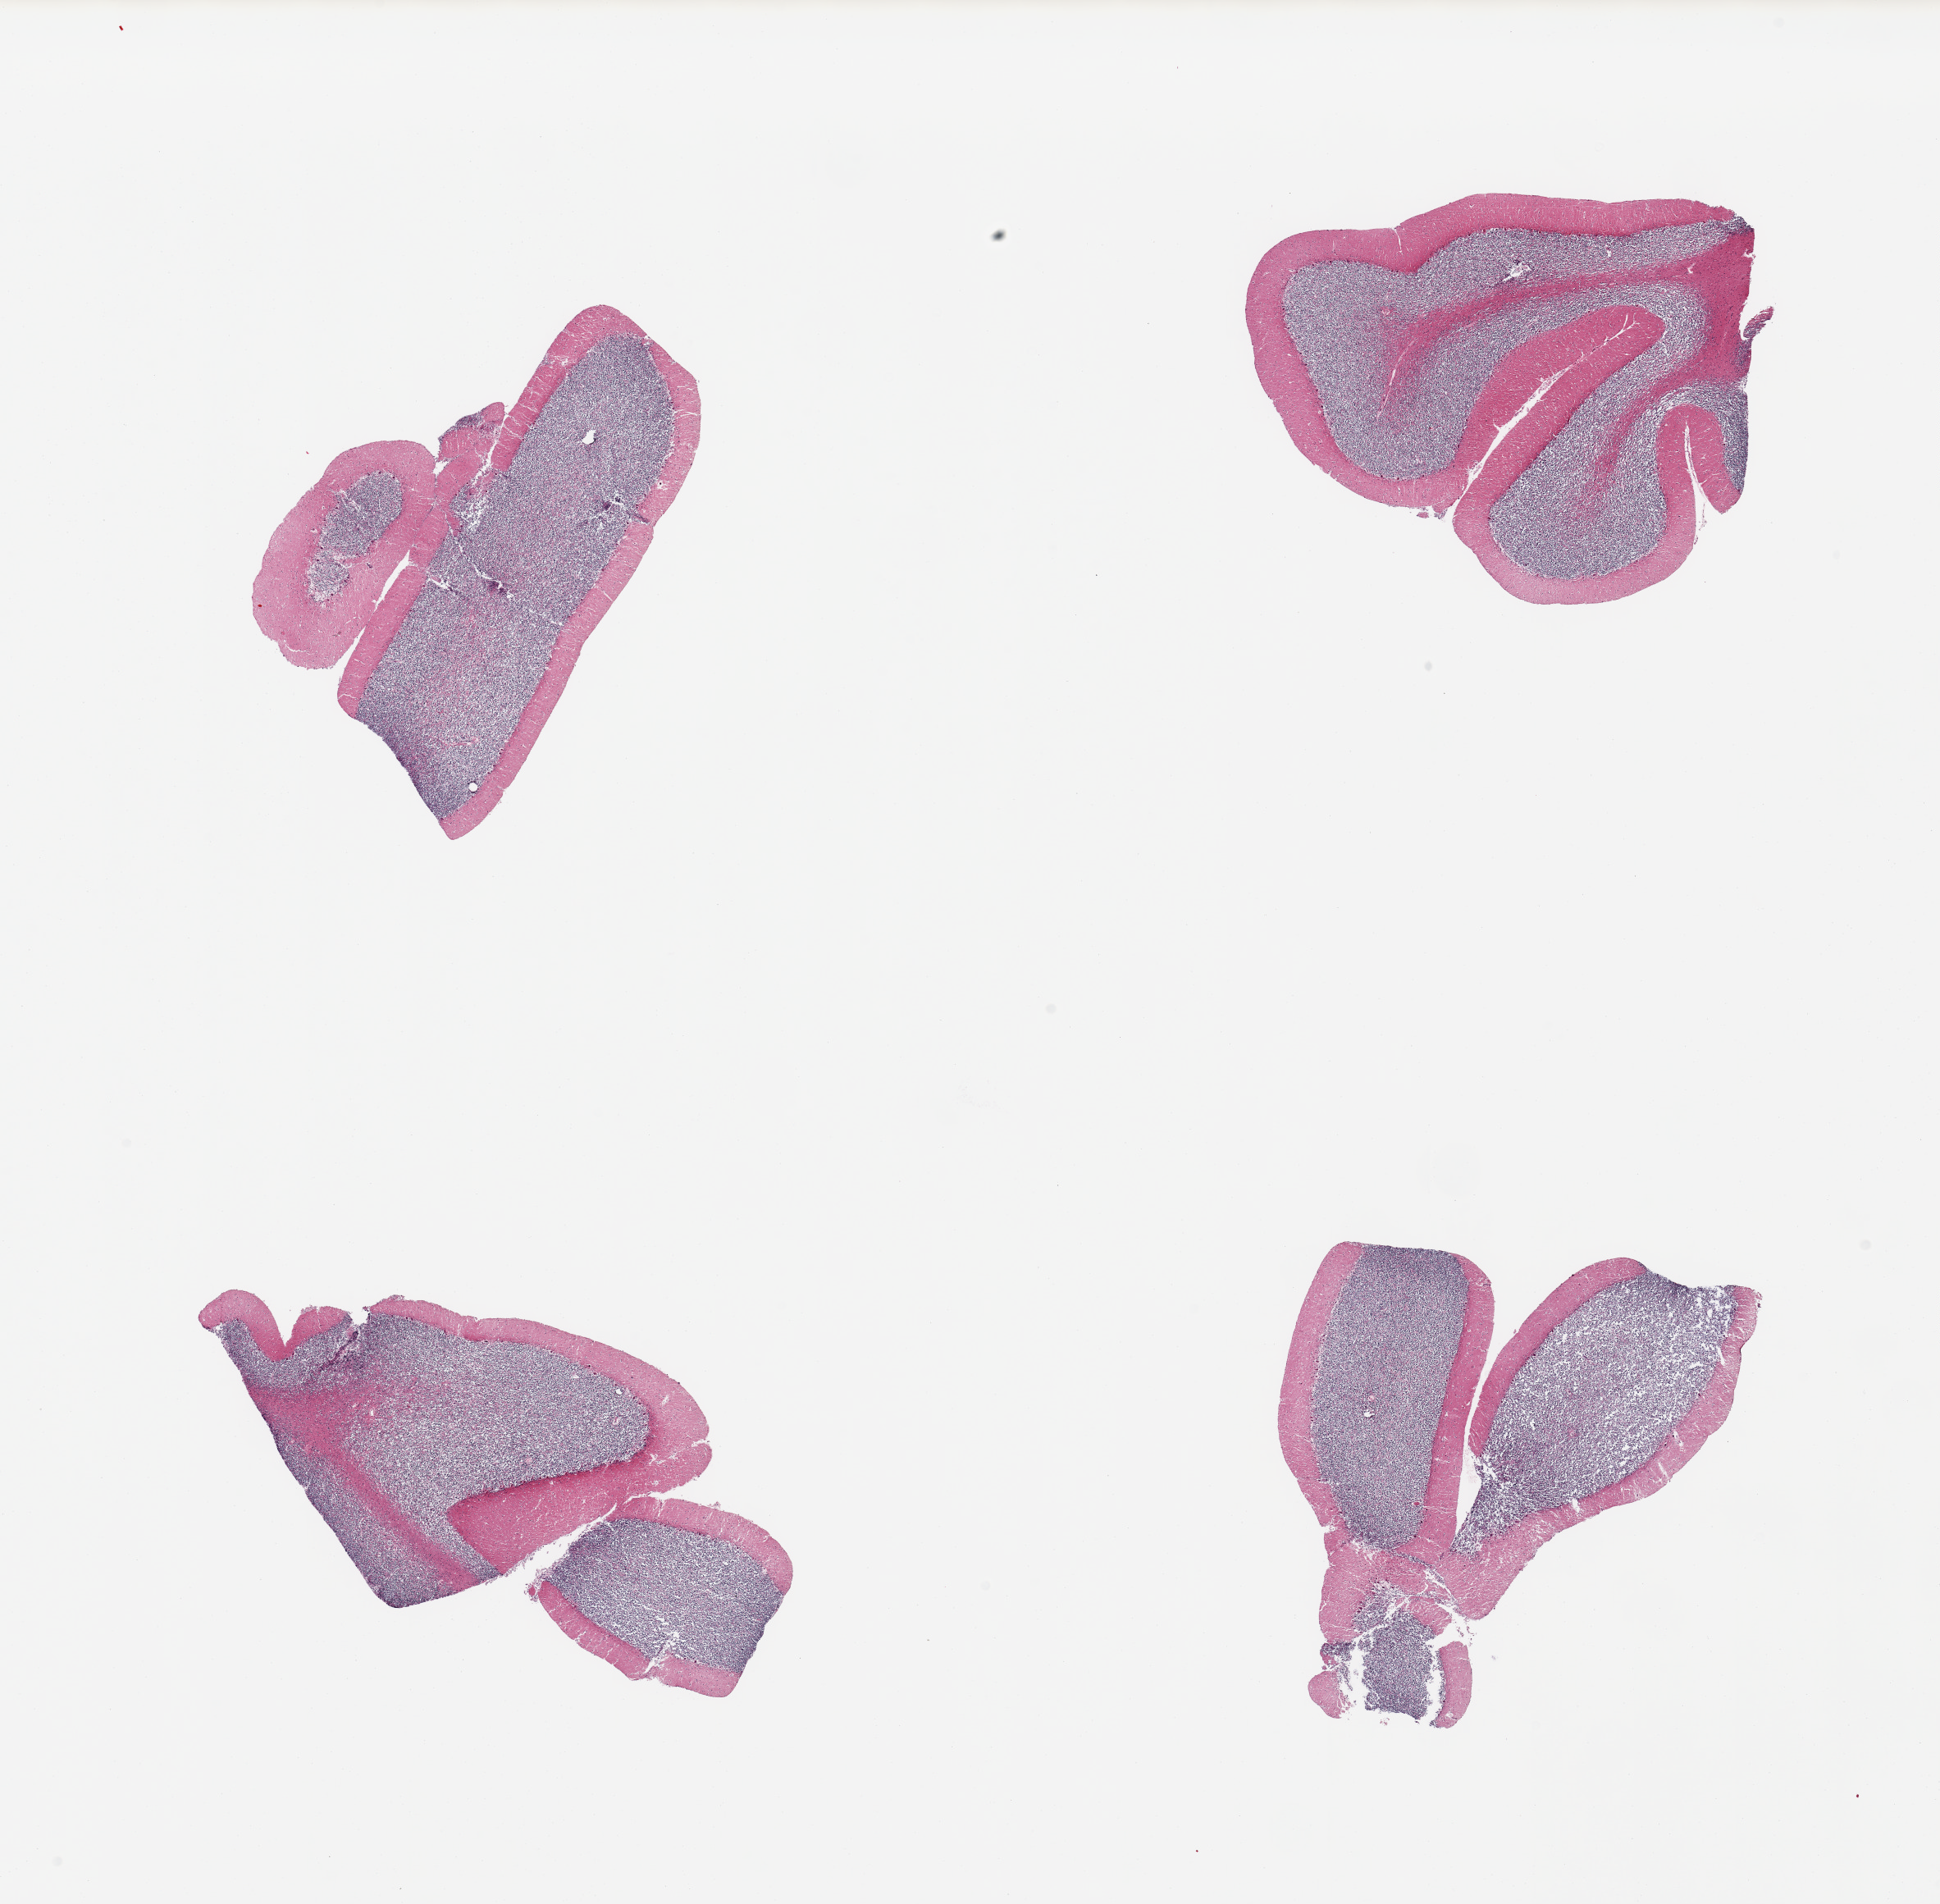
H&E whole-slide image — low-resolution overview of the scanned area, about 18.7 x 18.4 mm, PAXgene-fixed, paraffin-embedded tissue, section of cerebellum (target tissue), tissue donor sample.
Pathologist's review note for this sample: 4 pieces, no abnormalities.